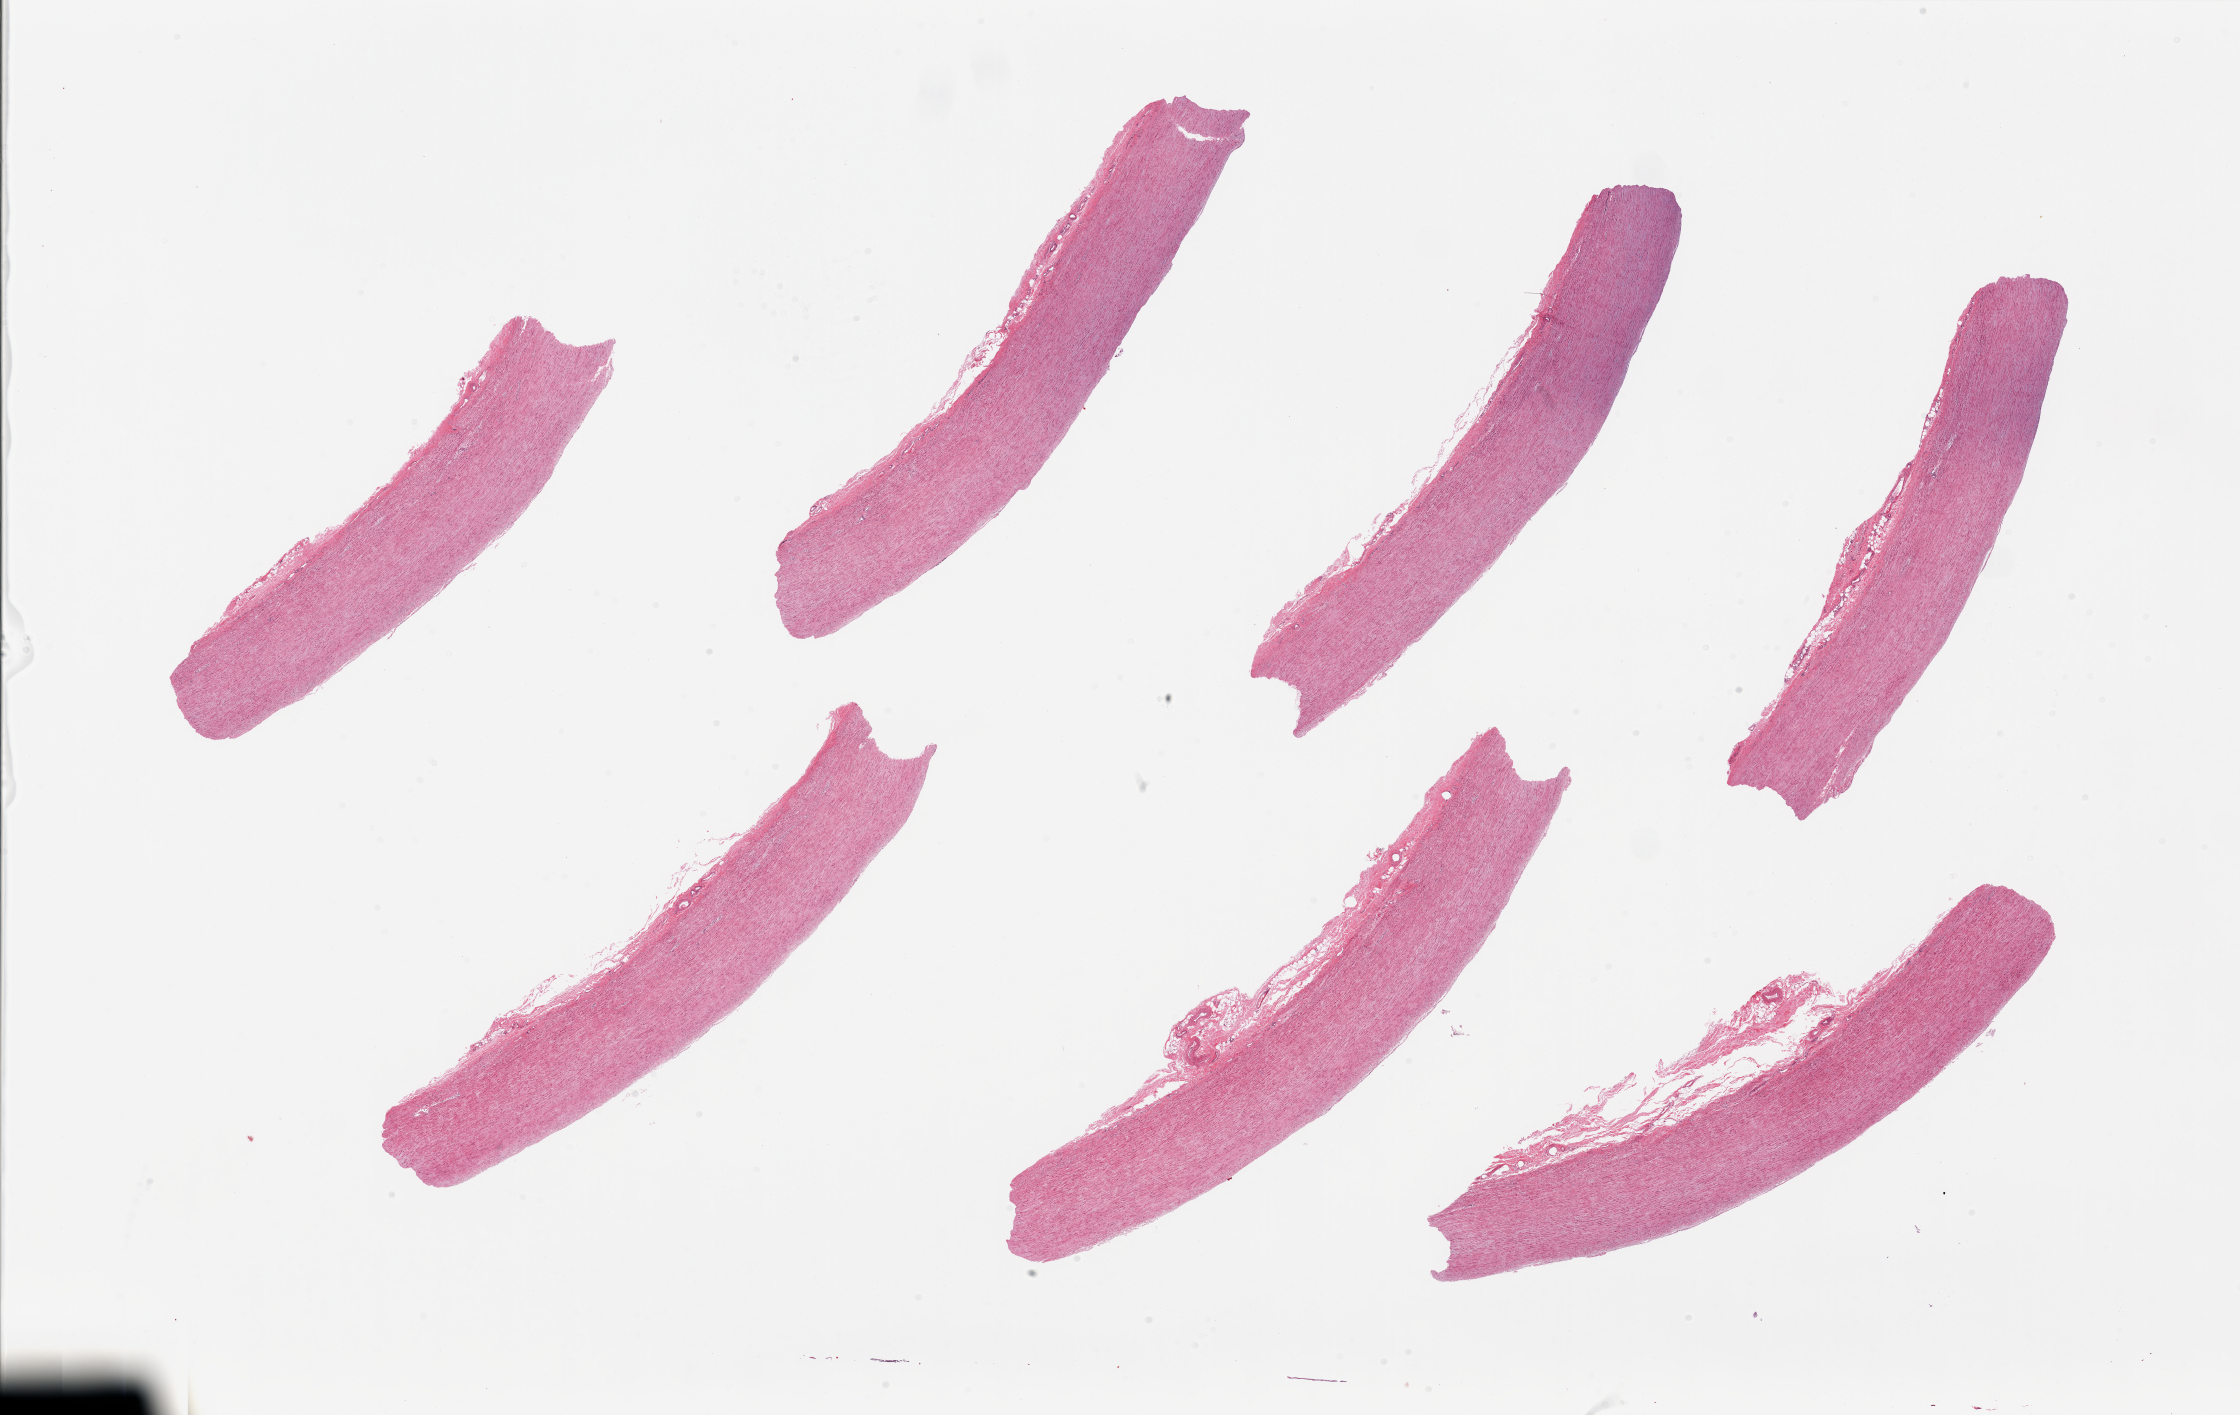
Whole-slide image, haematoxylin and eosin stain — a low-resolution overview of the entire scanned area, about 35.4 x 22.4 mm (from a 20x scan); PAXgene-fixed paraffin-embedded (PFPE) section; sampled site (target tissue): aorta; donor tissue sample. Donor sex: female.
Review note (as recorded): 7 pieces.